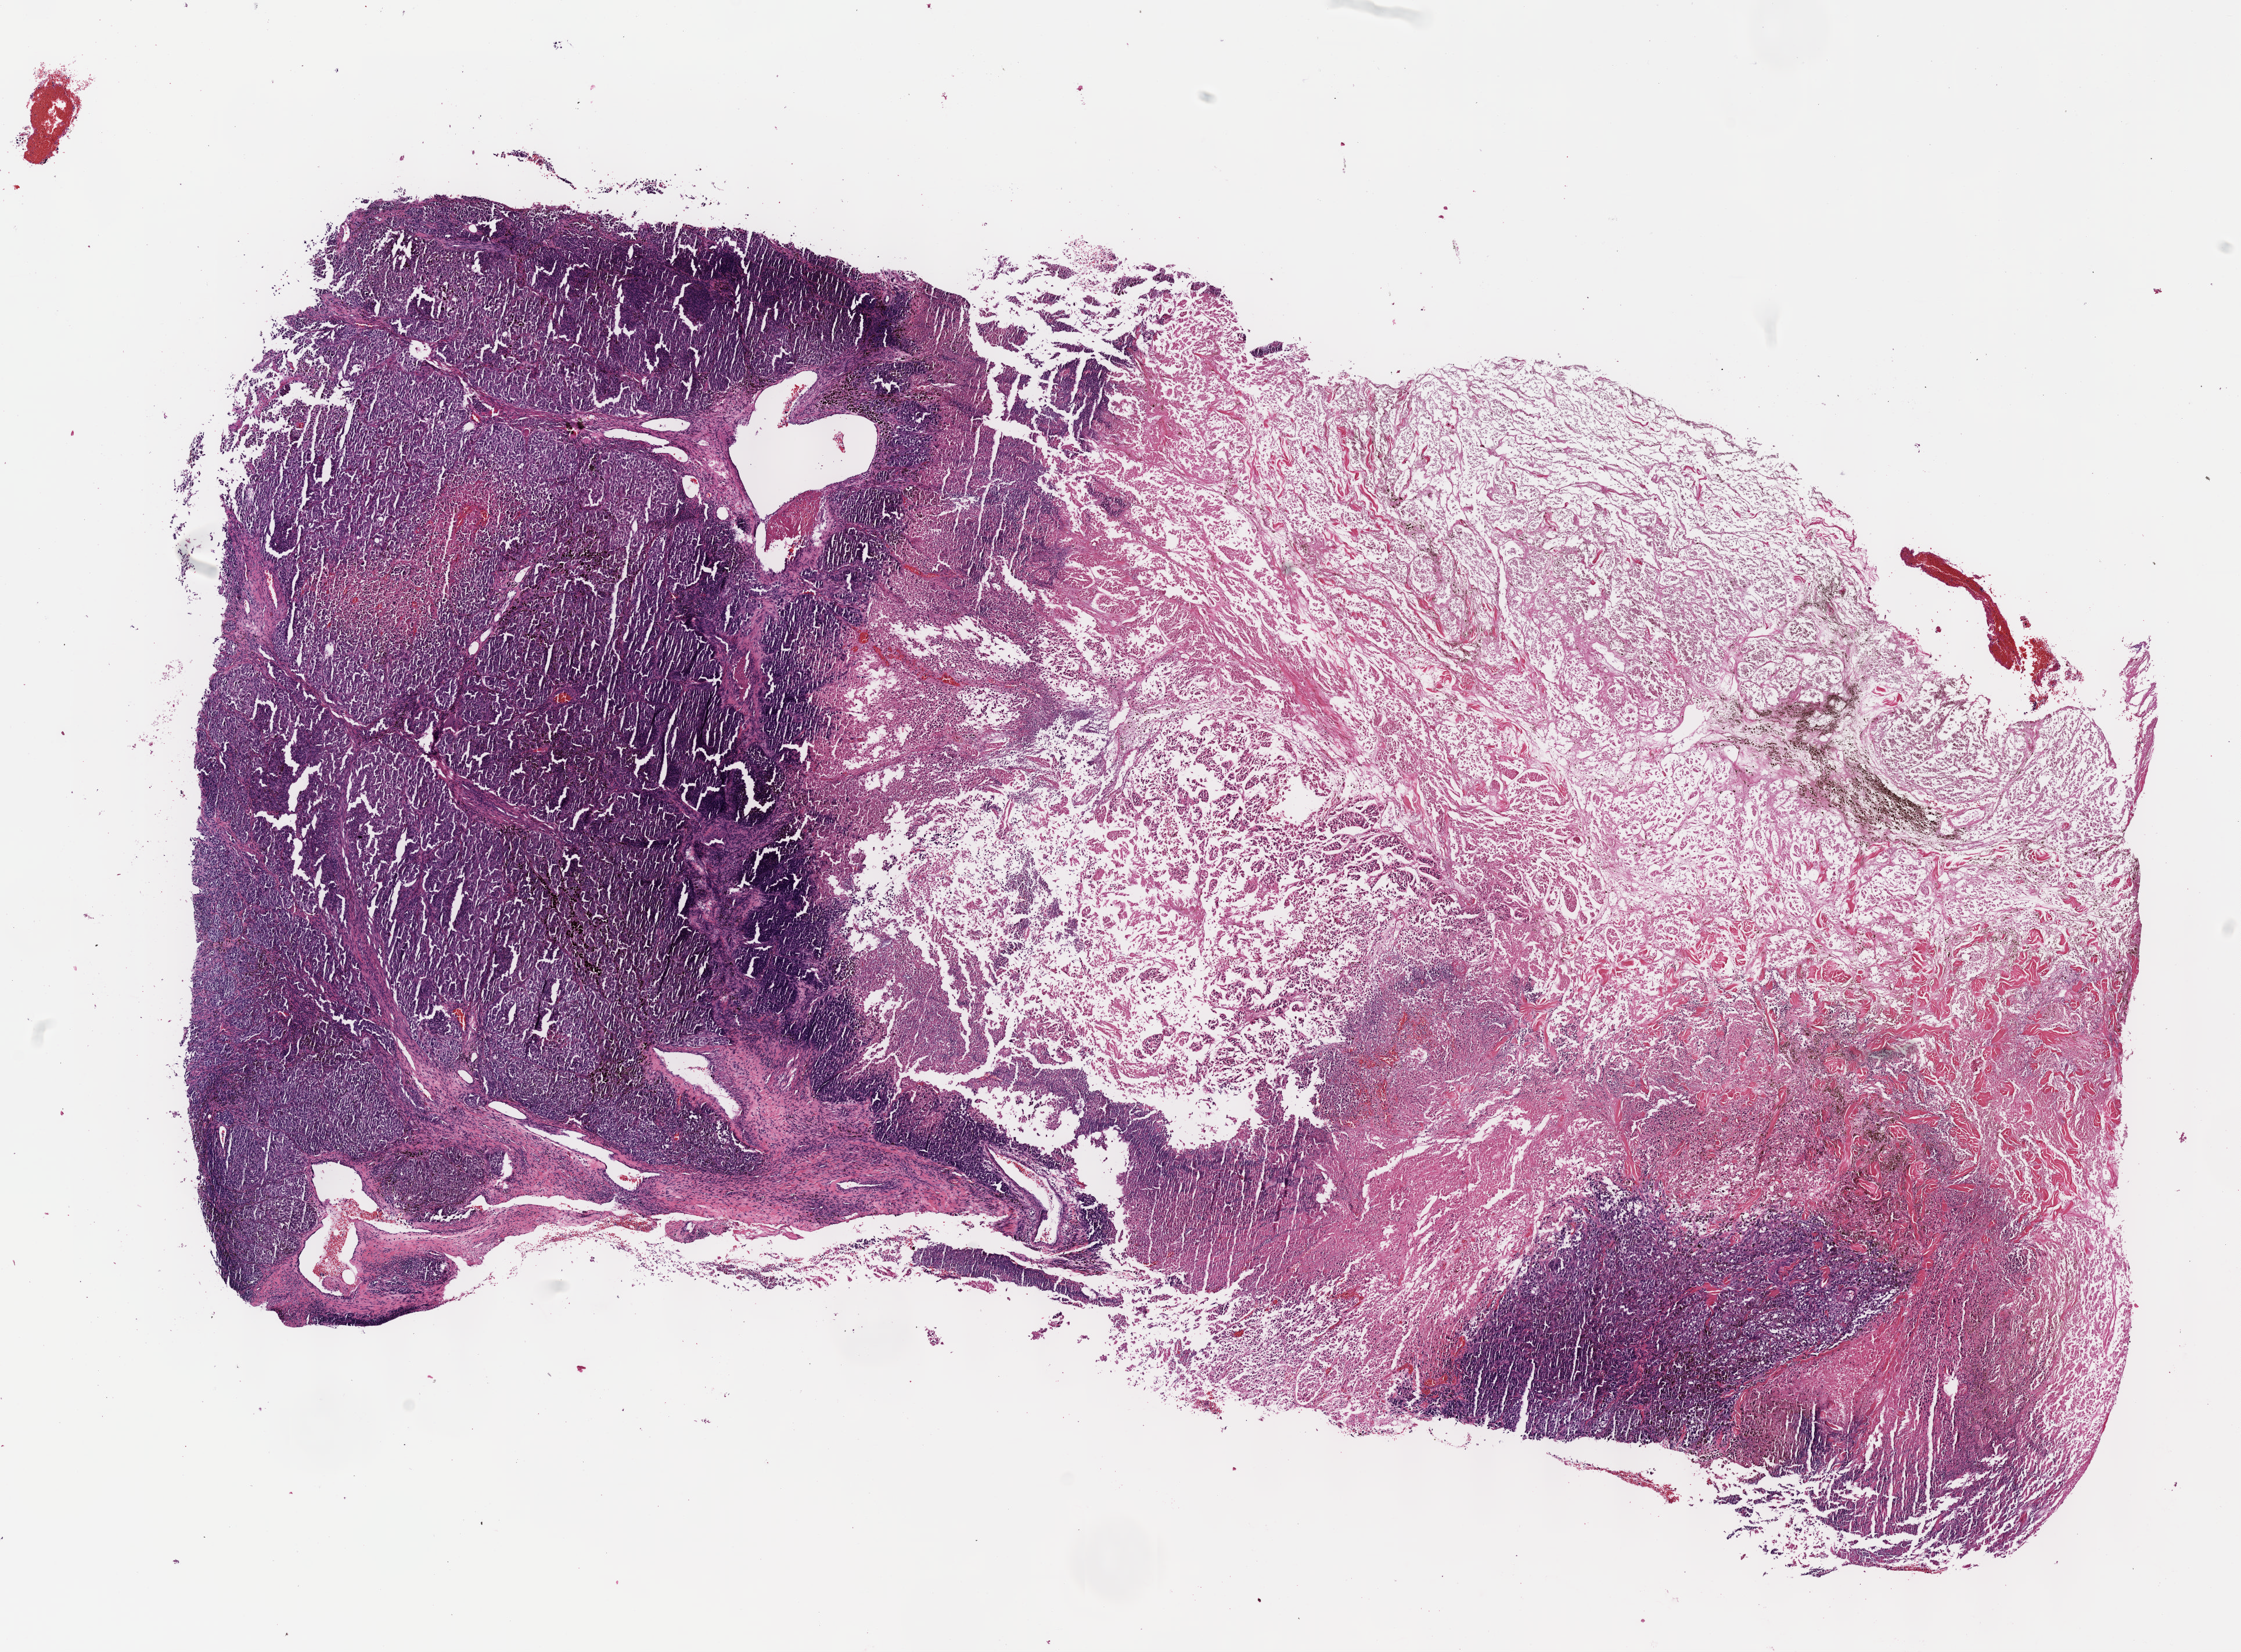
H&E-stained whole-slide image, whole scanned area (about 15.6 x 11.5 mm, acquisition: 40x scan) shown as a low-resolution overview. Formalin-fixed paraffin-embedded (FFPE) diagnostic section. Skin, primary tumour sample. Female, age 75 years at initial diagnosis.
- diagnosis: Malignant melanoma, NOS
- AJCC pathologic stage: IIIC (7th edition)